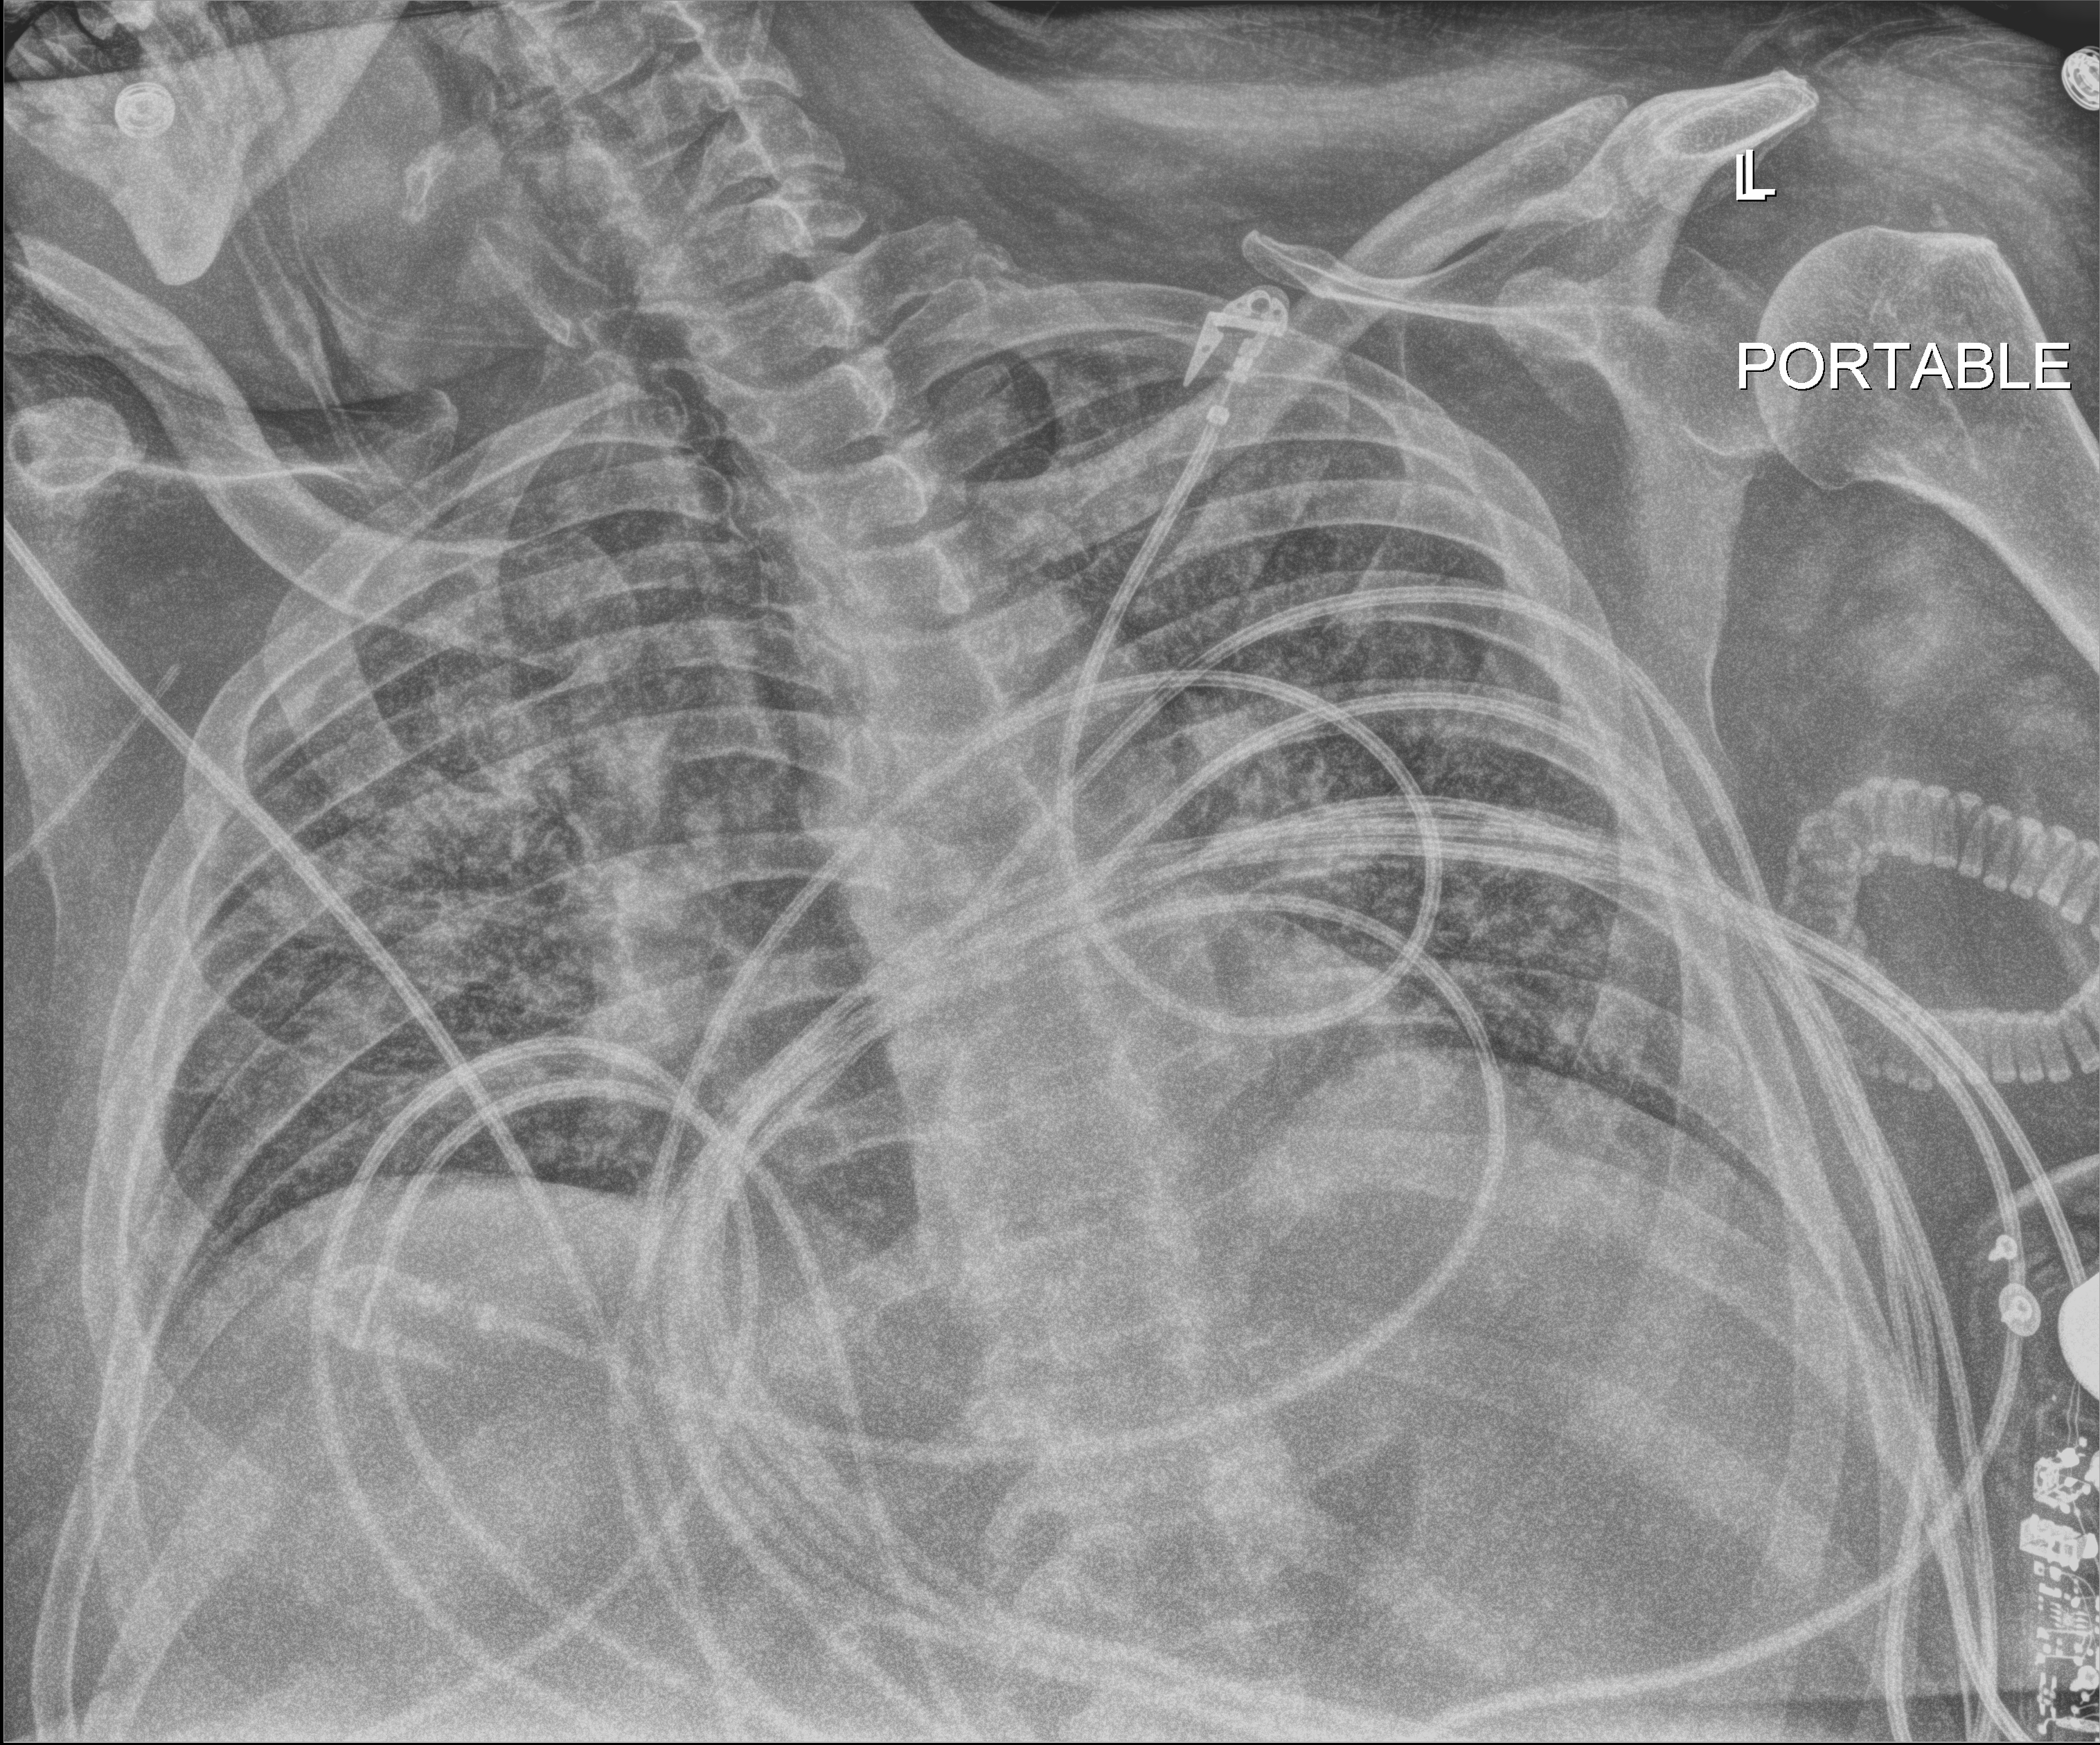
Chest X-ray (portable). Male patient hospitalised with COVID-19, age 60–74 years.
From the hospital-stay record, not from the radiograph (when in the stay this image was taken is not recorded):
- other chronic lung disease (admission record): no
- mechanically ventilated during this hospital stay: yes
- admitted to intensive care during this hospital stay: yes